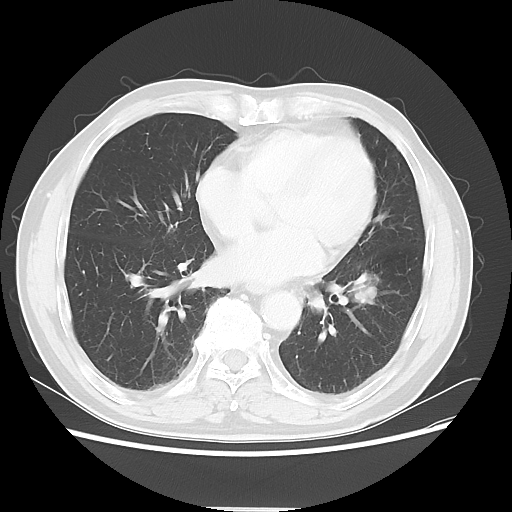
Chest CT, one axial slice. Position 23 of 64 along the scan axis. Reconstruction kernel LUNG. 120 kVp. Lung window (W 1500 / L -600 HU). 5 mm slice thickness. 512 × 512 image matrix. Male patient, age 71 years. From the clinical record (not read from this slice): clinical TNM (as recorded): T1c N1 M0; histopathological grade: G2-3.
Annotated regions visible in this slice (rectangle marked by the reading radiologist):
- lung tumour (recorded histology: adenocarcinoma): bounding box (x1, y1, x2, y2) in pixels: (342, 261, 381, 309)